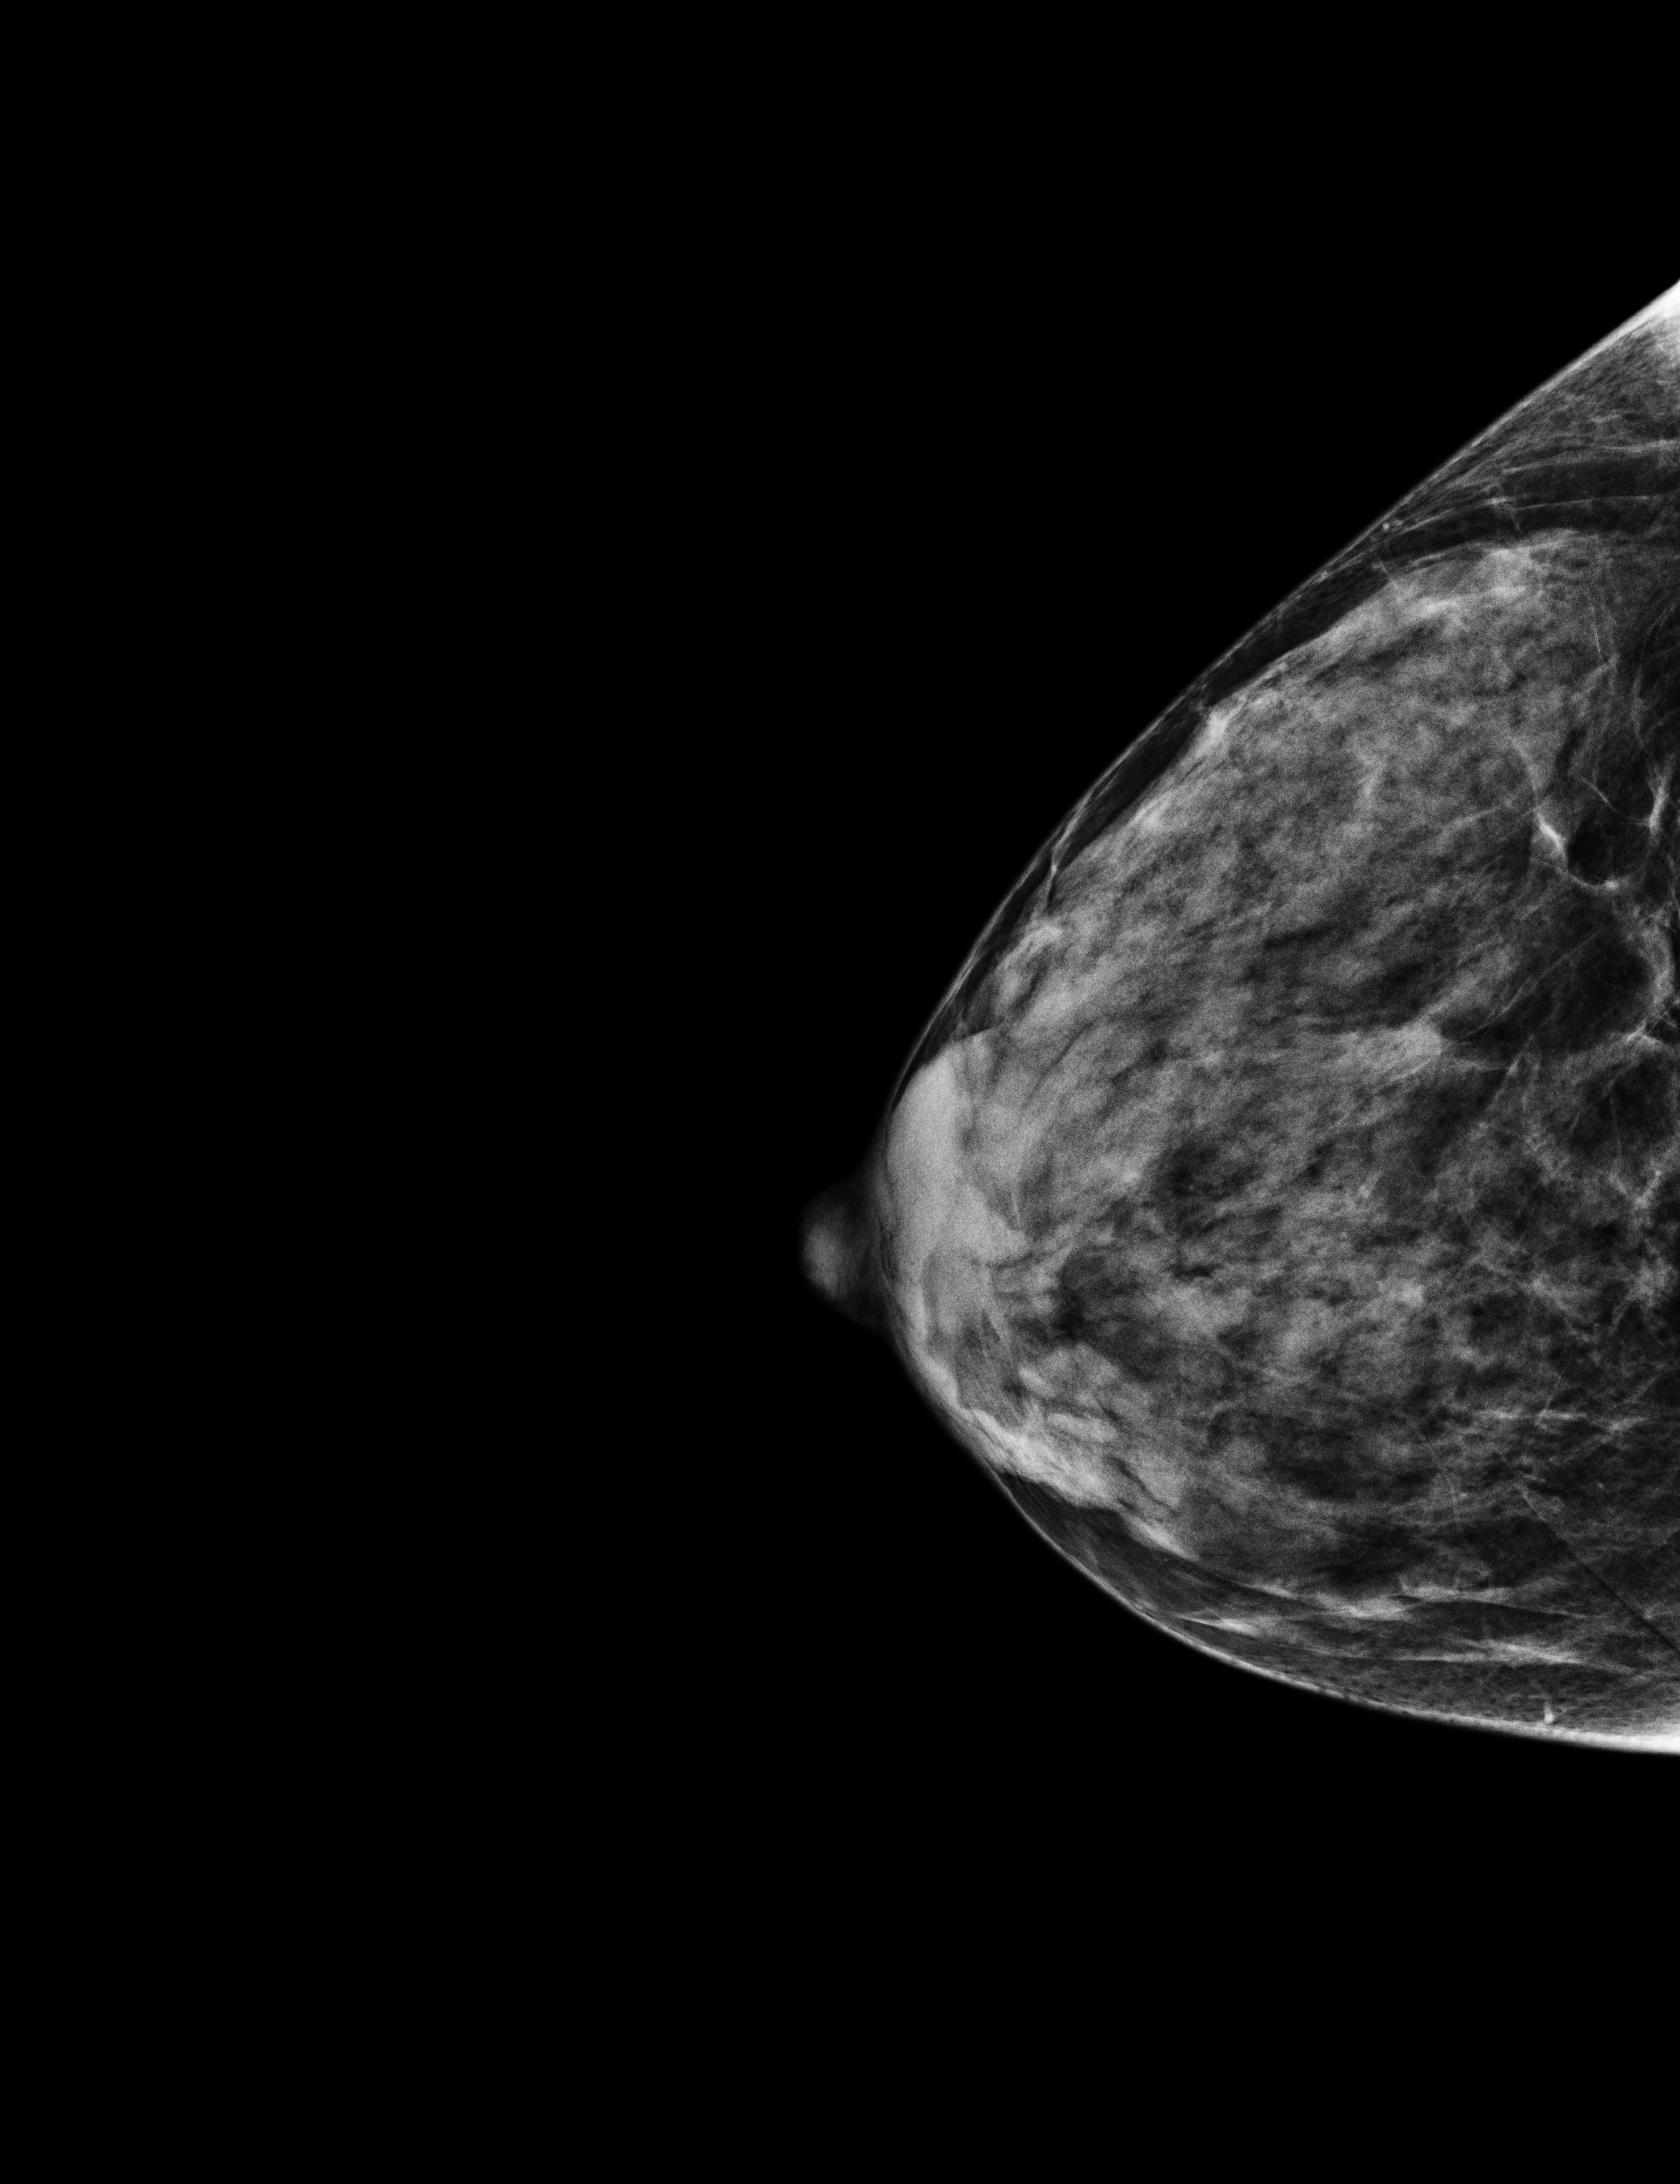
Full-field digital mammogram (FFDM); right breast; craniocaudal (CC) view; annual screening mammography examination; compressed breast thickness 27 mm; system: Selenia Dimensions. Female patient, age 55 years.
Breast density at the screening exam (both breasts): heterogeneously dense (BI-RADS density category c). Final BI-RADS category for the screening round (tomosynthesis exam, both breasts): category 2. Recall: no recall after this screen.